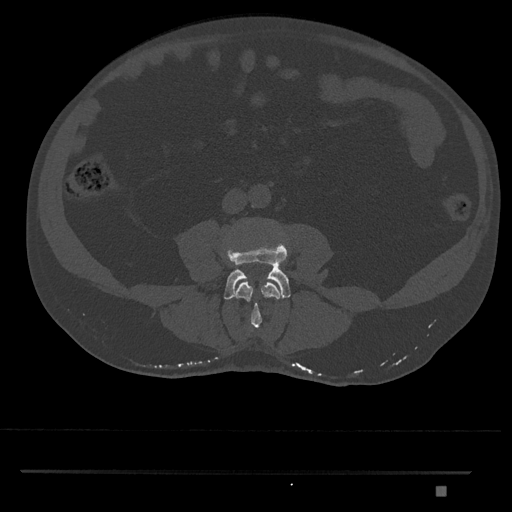
CT including the spine, one axial slice. Position 644 of 1134 along the scan axis. Reconstruction kernel Br40s/3. 120 kVp. Bone window (W 1800 / L 400 HU). 0.5 mm slice thickness. 512 × 512 image matrix. Patient: male, 65 years. Case-level facts recorded for this patient, not image findings: primary cancer: prostate.
Outlined on this slice (semi-automatic segmentation, software-assisted and operator-edited):
- L3 vertebra: bounding box <235,282,280,332> (left, top, right, bottom; pixels)
- L4 vertebra: <223,235,291,300>